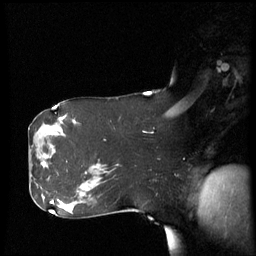
Breast MRI (dynamic contrast-enhanced), one sagittal slice. Slice 36 of 60 in the series (ordered by position). Dynamic contrast-enhanced series, image 2 of 3 at this slice position (ordered by acquisition). 1.5 T. TE 4.2 ms, TR 8.4 ms. 2.9 mm slice thickness. 256 × 256 image matrix, field of view 280 × 280 mm. Female patient, age 61 years. Case-level facts recorded for this patient, not image findings: setting: breast cancer imaged before/during neoadjuvant chemotherapy; receptor status: HR-positive, HER2-negative.
Annotated regions visible in this slice (semi-automatically segmented with operator editing):
- analysis volume of interest (the breast-tissue region the enhancement analysis was run in; not a lesion): box from (x=31, y=142) to (x=56, y=179) px
- tumour enhancement mask (voxels above the 70 % enhancement threshold inside the analysis volume of interest): (x=43, y=162)–(x=48, y=167)